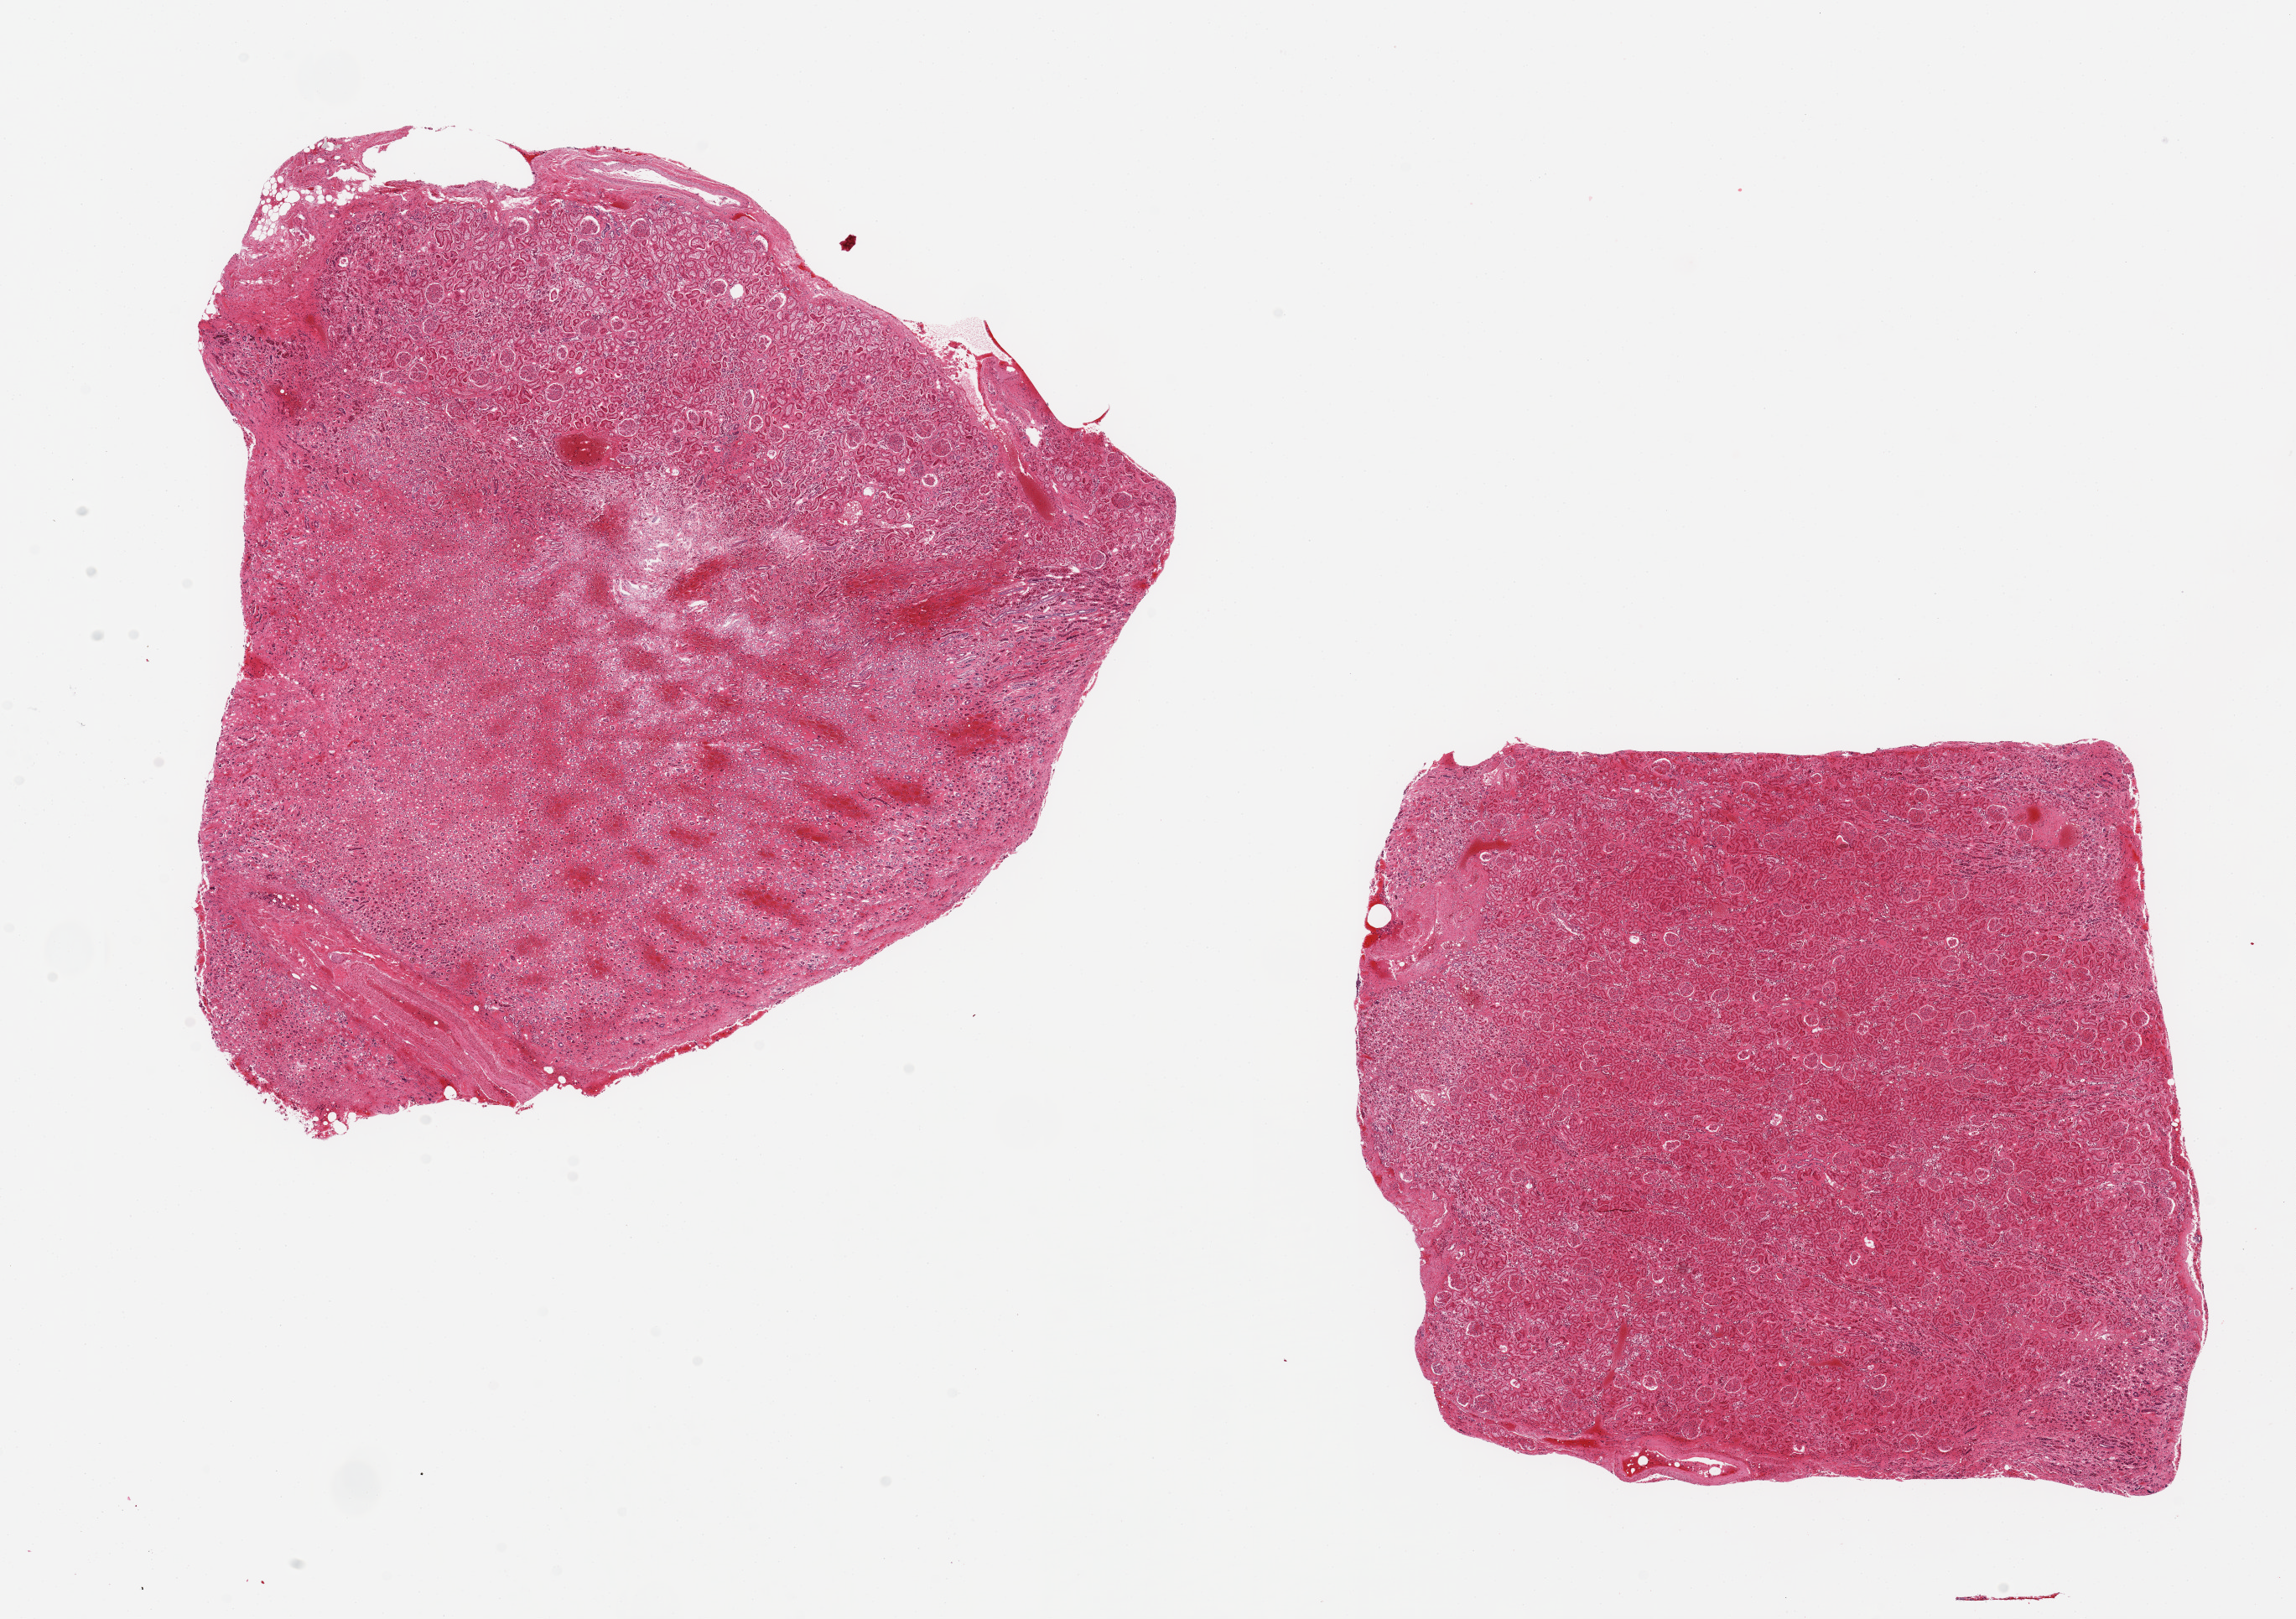
Haematoxylin and eosin whole-slide image, brightfield — whole scanned area (about 21.7 x 15.3 mm) shown as a low-resolution overview, PAXgene-fixed paraffin-embedded (PFPE) section, target tissue: renal medulla, tissue donor sample. Female donor.
Pathologist's review note for this sample: 2 pieces, 10x9 & 7x7 mm; 1 piece is >90% cortex; 1 piece is 75% medulla & 25% cortex; moderate congestion.